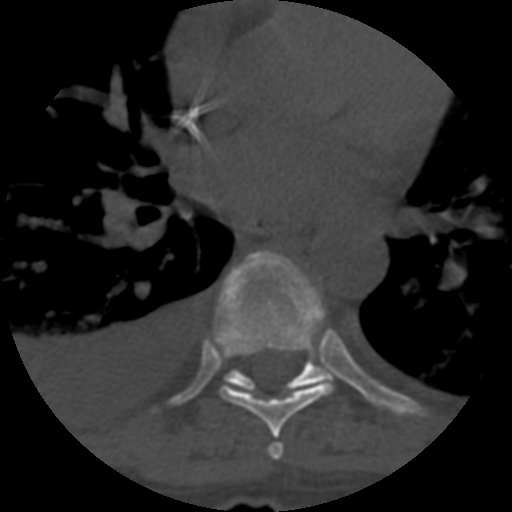
CT including the spine, one axial slice. Slice 409 of 708 in the series (ordered by position). Reconstruction kernel STANDARD. 120 kVp. One of 3 acquisitions stored at this slice position. Bone window (W 1800 / L 400 HU). 1.25 mm slice thickness. 512 × 512 image matrix. Patient age 55 years. Case-level facts recorded for this patient, not image findings: primary cancer: colon; vertebrae with lytic lesions (as recorded): T12, L1, L5.
Outlined on this slice (semi-automatically segmented with operator editing):
- T6 vertebra: bounding box <268,443,284,460> (left, top, right, bottom; pixels)
- T7 vertebra: <215,253,334,438>
- T8 vertebra: <224,348,330,395>